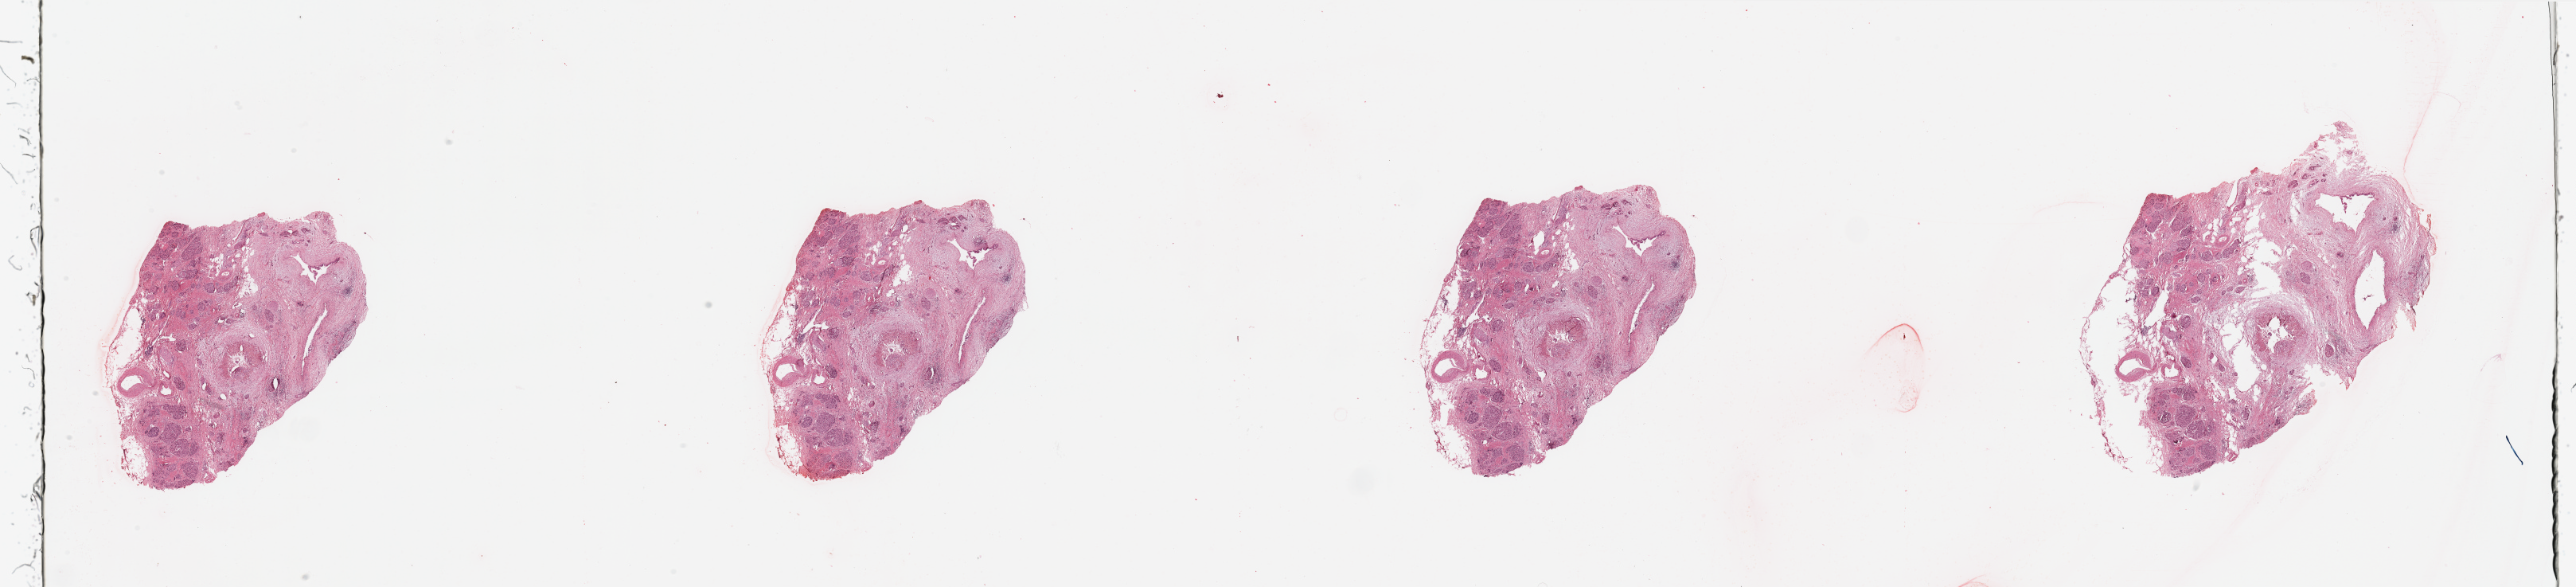
Whole-slide histology image, H&E, a low-resolution overview of the entire scanned area, about 51.2 x 11.7 mm (from a 20x scan), normal (non-tumour) tissue sample, pancreas. 72-year-old male patient.
- this section: normal (non-tumour) tissue from the same patient
- patient diagnosis: Infiltrating duct carcinoma, NOS